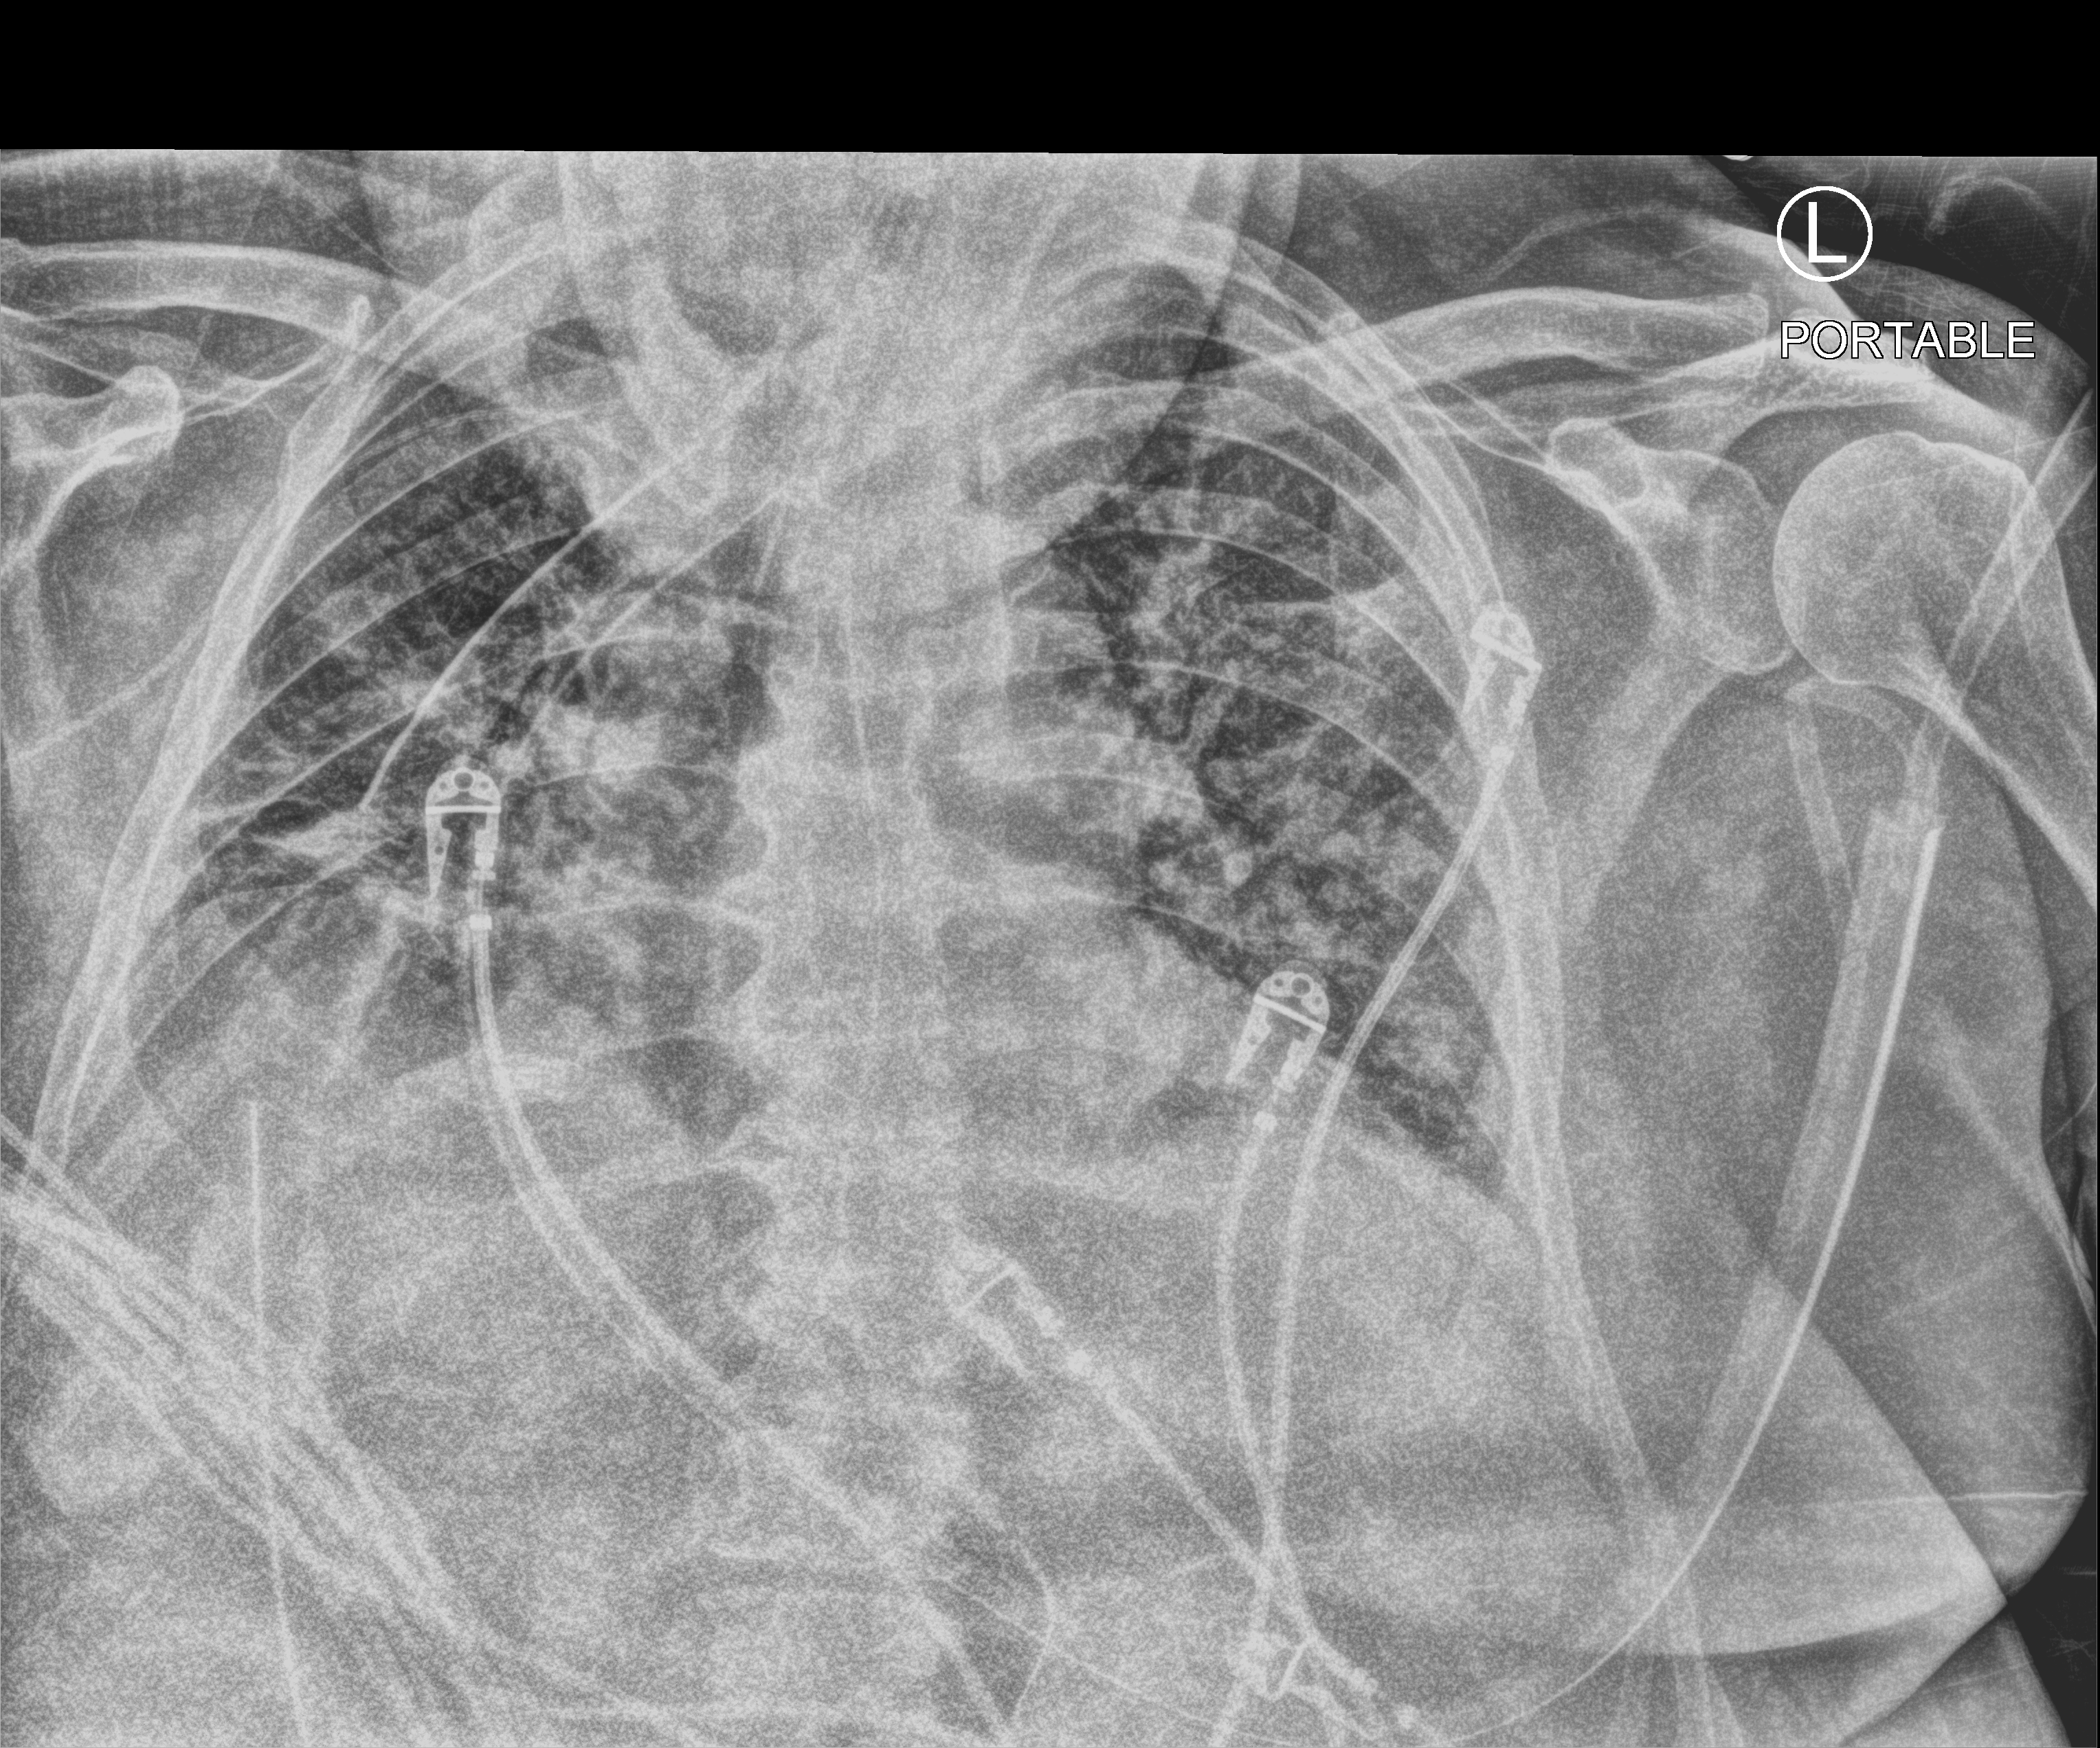
Portable chest radiograph. Male patient hospitalised with COVID-19, age 60–74 years.
Hospital-stay facts (about this admission, not read from this image; timing relative to this image not recorded):
- length of hospital stay: 26 days
- hypertension (admission record): yes